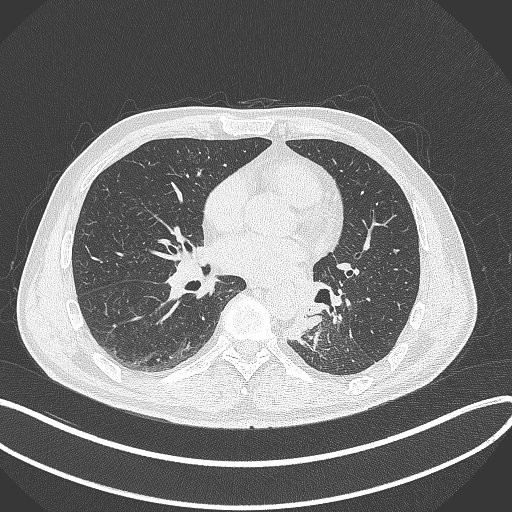
Chest CT, one axial slice; position 147 of 329 along the scan axis; reconstruction kernel B70f; 120 kVp; lung window (W 1500 / L -600 HU); 1 mm slice thickness; 512 × 512 image matrix. Male patient, age 59 years. From the clinical record (not read from this slice): clinical TNM (as recorded): T2a N2 M0.
Outlined on this slice (rectangle marked by the reading radiologist):
- lung tumour (recorded histology: squamous cell carcinoma): box from (x=281, y=310) to (x=326, y=344) px